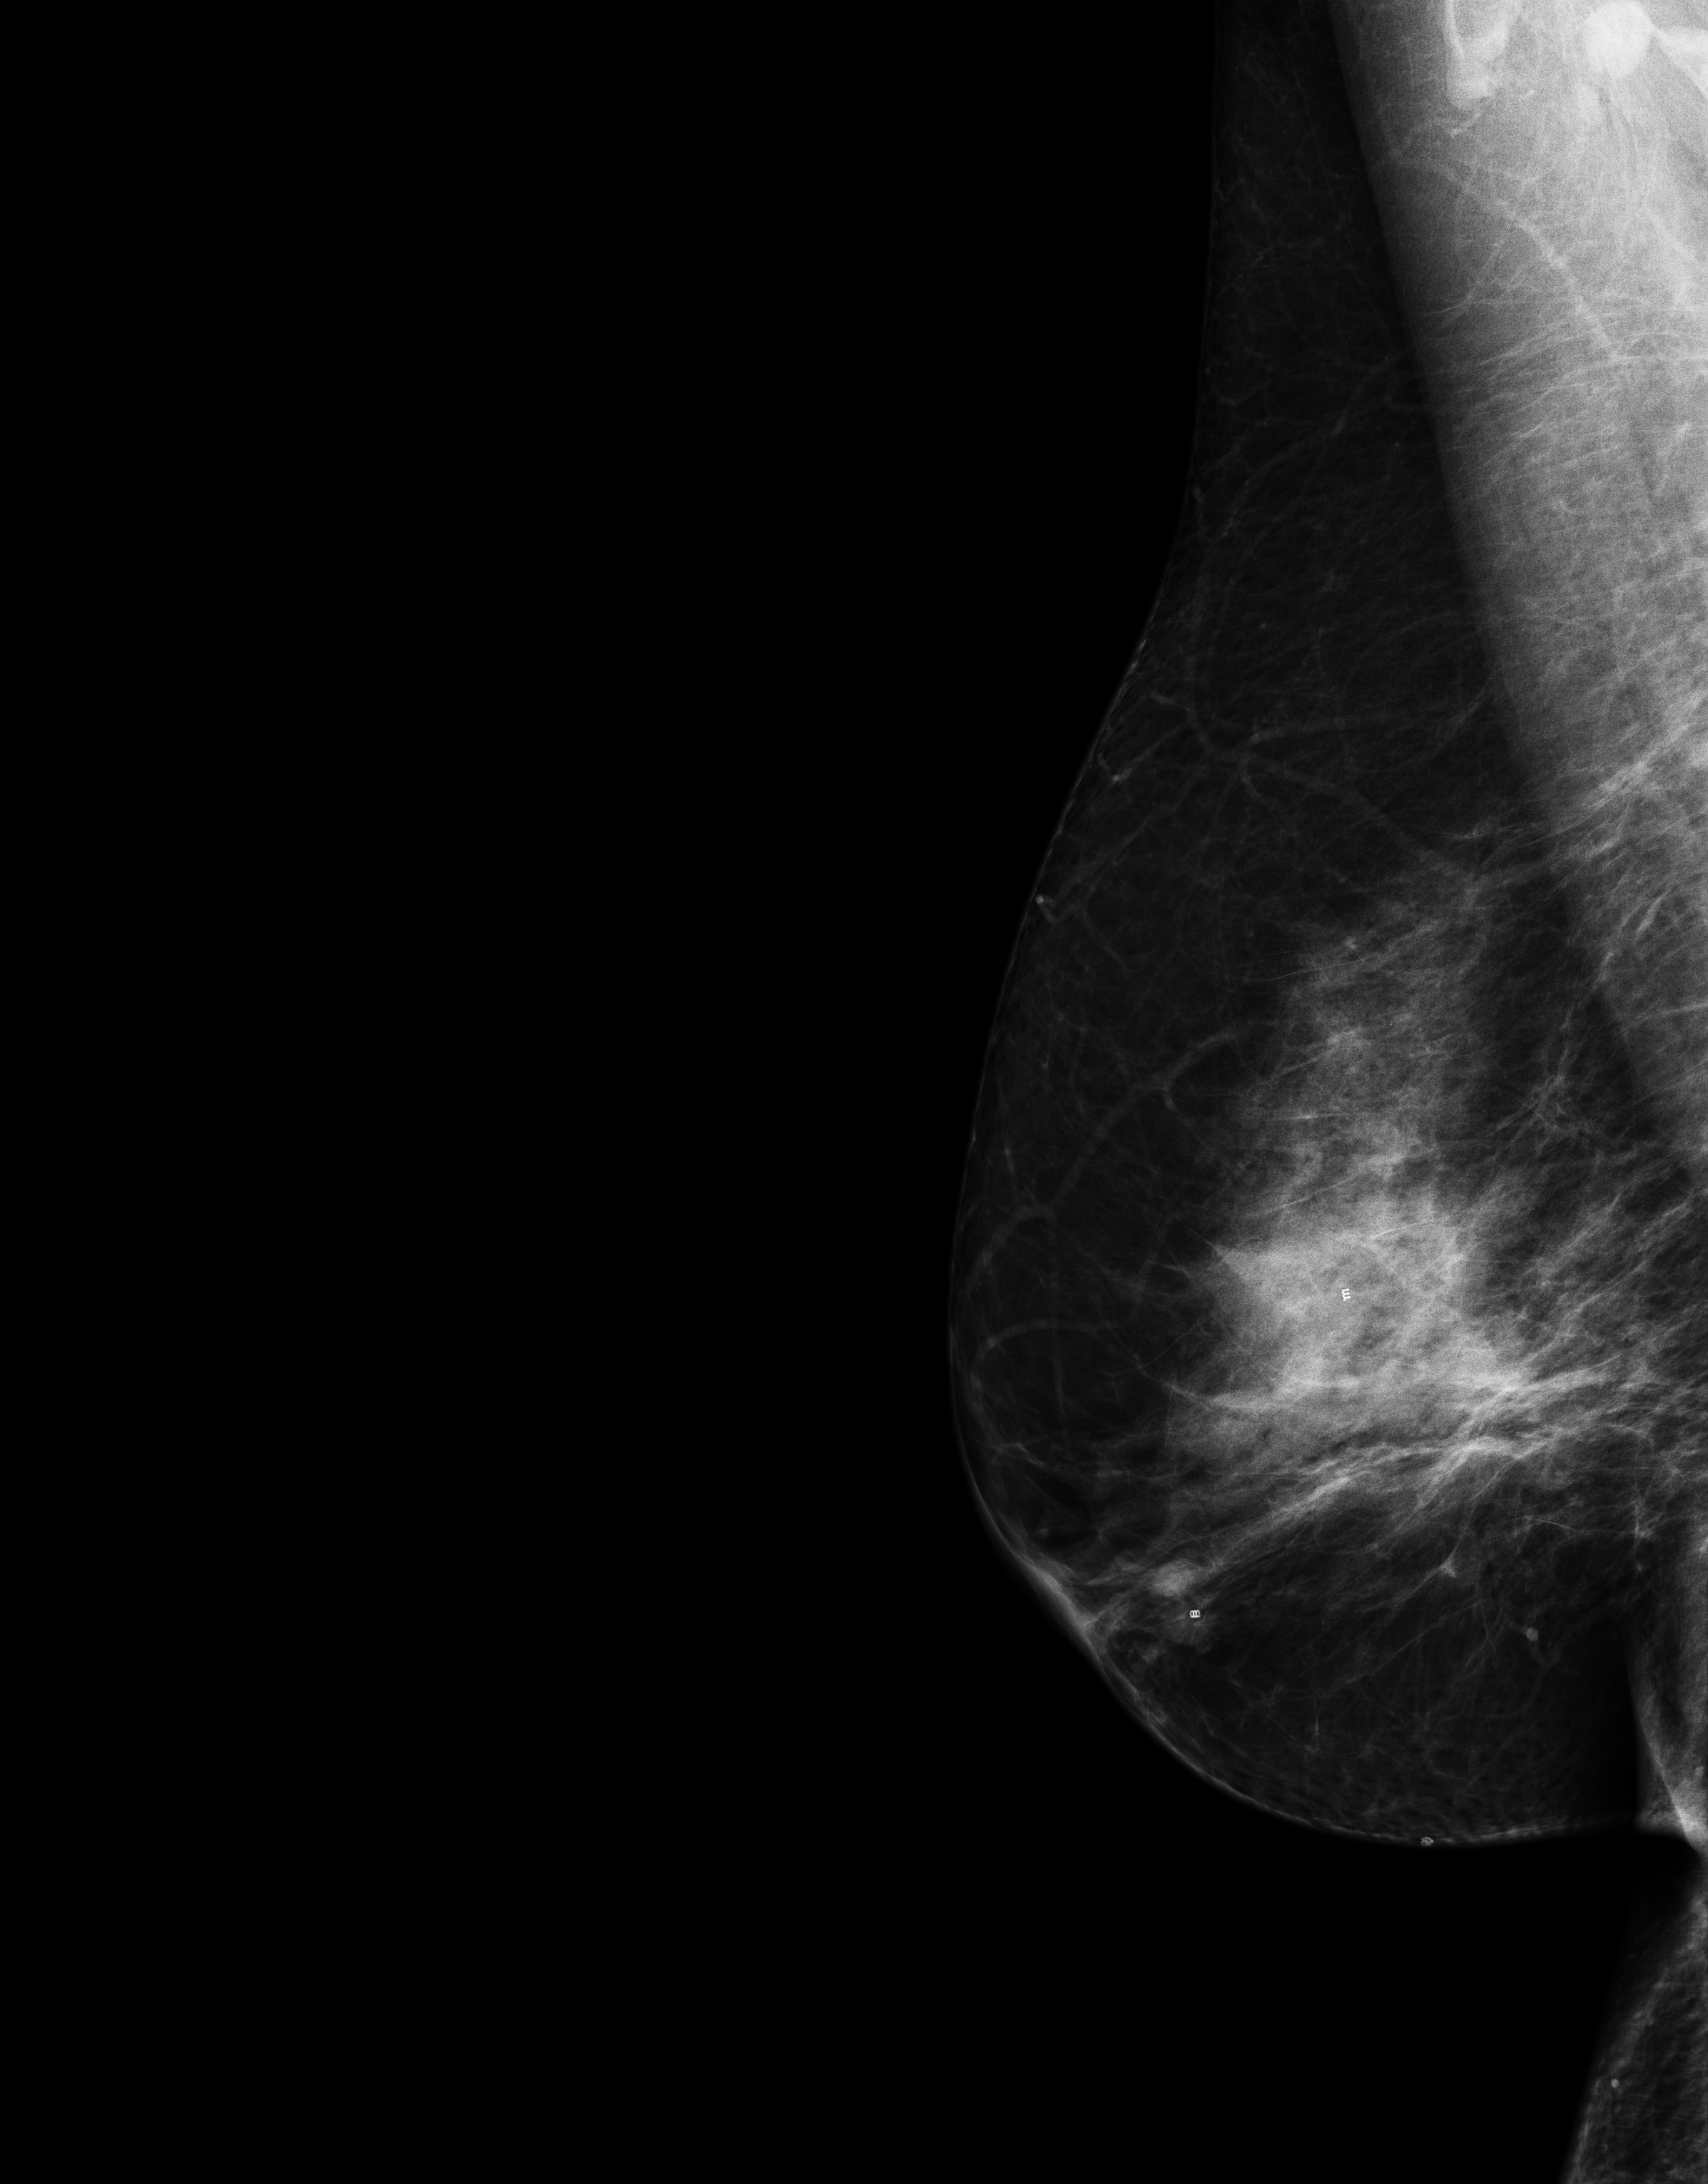
Digital mammogram (FFDM); right breast; MLO view; screening examination. Female patient, age 47 years.
BI-RADS breast density category at the screening exam (both breasts, scale 1–4): 3. Final BI-RADS assessment for this screening round (tomosynthesis exam, both breasts): category 1. Recall: no recall after this screen.